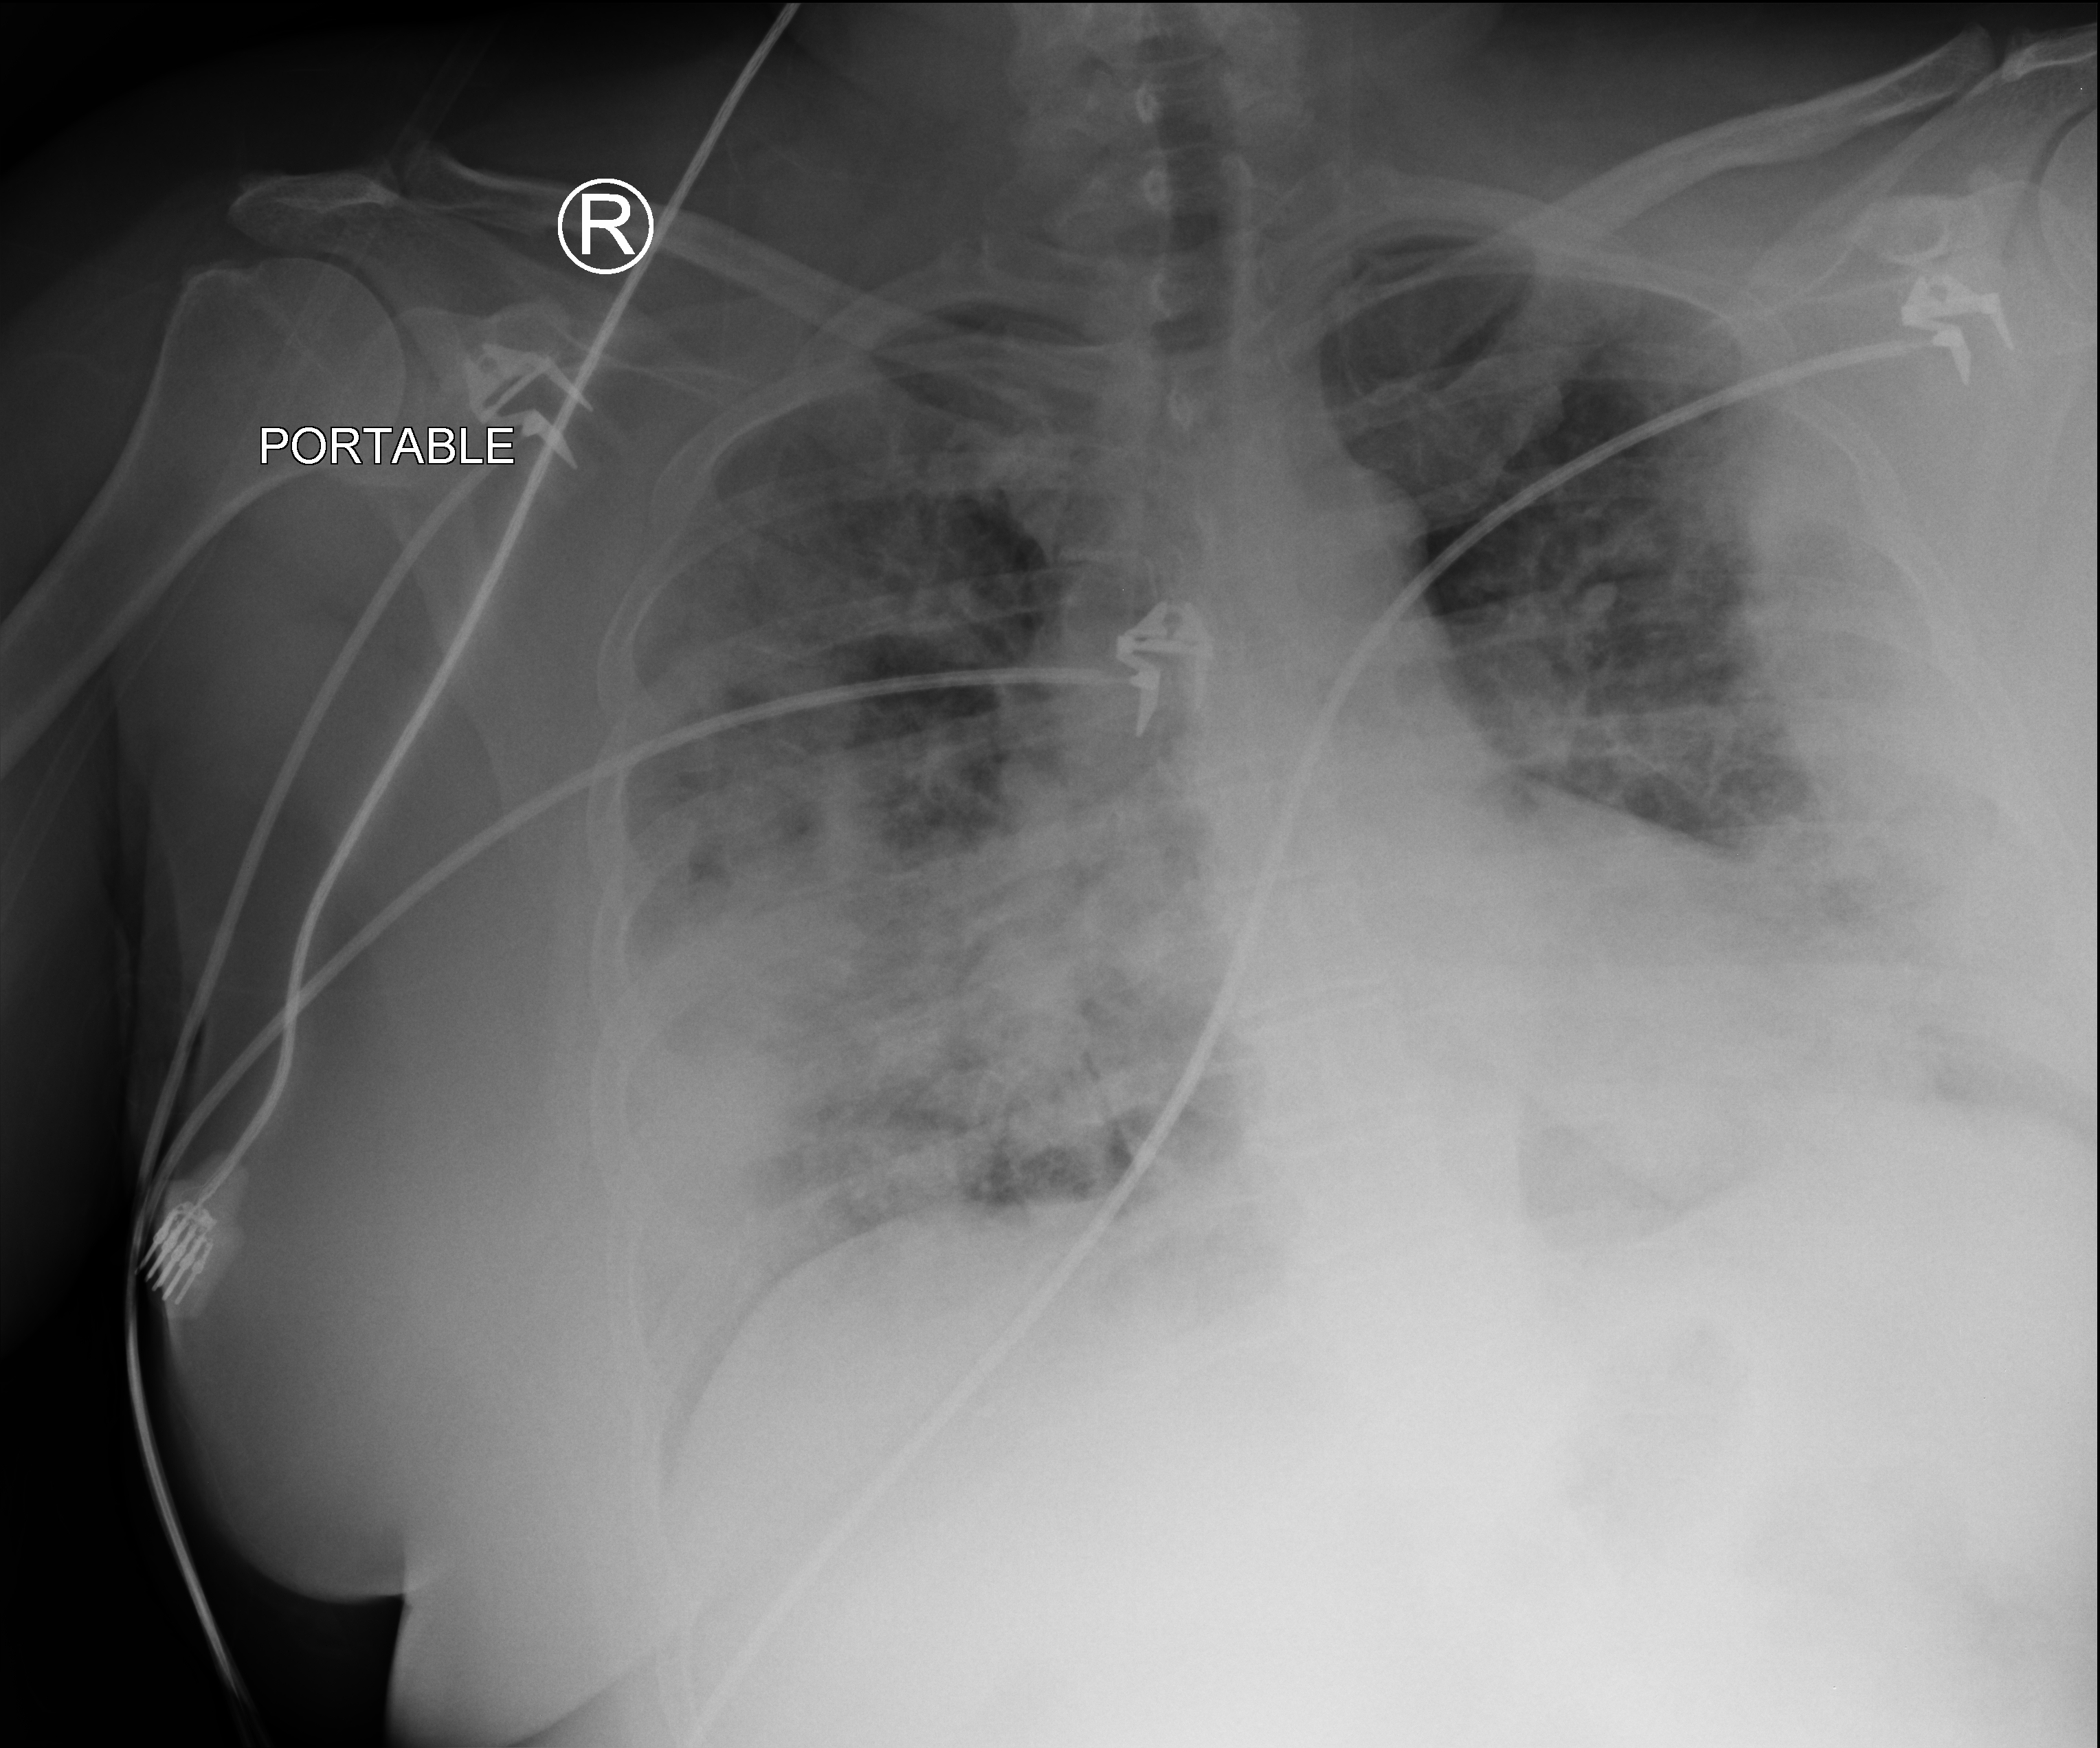
Chest X-ray (portable); anteroposterior (AP) projection. Patient hospitalised with COVID-19; female, aged 18–59 years.
Hospital-stay facts (about this admission, not read from this image; timing relative to this image not recorded): smoking status (admission record): current; other chronic lung disease (admission record): no; mechanically ventilated during this hospital stay: no.